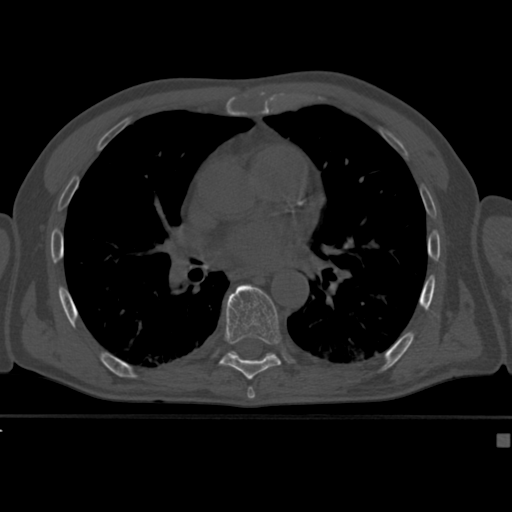
CT including the spine, one axial slice; slice 262 of 430 in the series (ordered by position); 120 kVp; bone window (W 1800 / L 400 HU); 512 × 512 image matrix, field of view 337 × 337 mm. Patient: male, 64 years. From the clinical record (not read from this slice): primary cancer: uterus; vertebrae with lytic lesions (as recorded): T1, T4, T5, T7, L5.
Structures marked on this image (semi-automatically segmented with operator editing):
- T8 vertebra: bounding box <219,284,281,382> (left, top, right, bottom; pixels)
- T9 vertebra: <229,351,275,359>